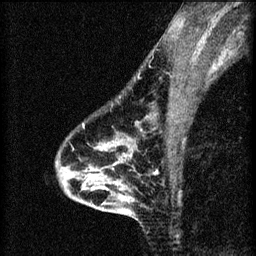
Breast MRI (dynamic contrast-enhanced), one sagittal slice; slice 45 of 60 in the series (ordered by position); 3 images stored at this slice position (order not interpretable as contrast timing); 1.5 T; TE 4.2 ms, TR 8.2 ms; 2 mm slice thickness; 256 × 256 image matrix, field of view 180 × 180 mm. Patient: female, 46 years.
Structures marked on this image (semi-automatic segmentation, software-assisted and operator-edited):
- analysis volume of interest (the breast-tissue region the enhancement analysis was run in; not a lesion): box from (x=55, y=116) to (x=148, y=209) px
- tumour enhancement mask (voxels above the 70 % enhancement threshold inside the analysis volume of interest): (x=83, y=124)–(x=92, y=181)